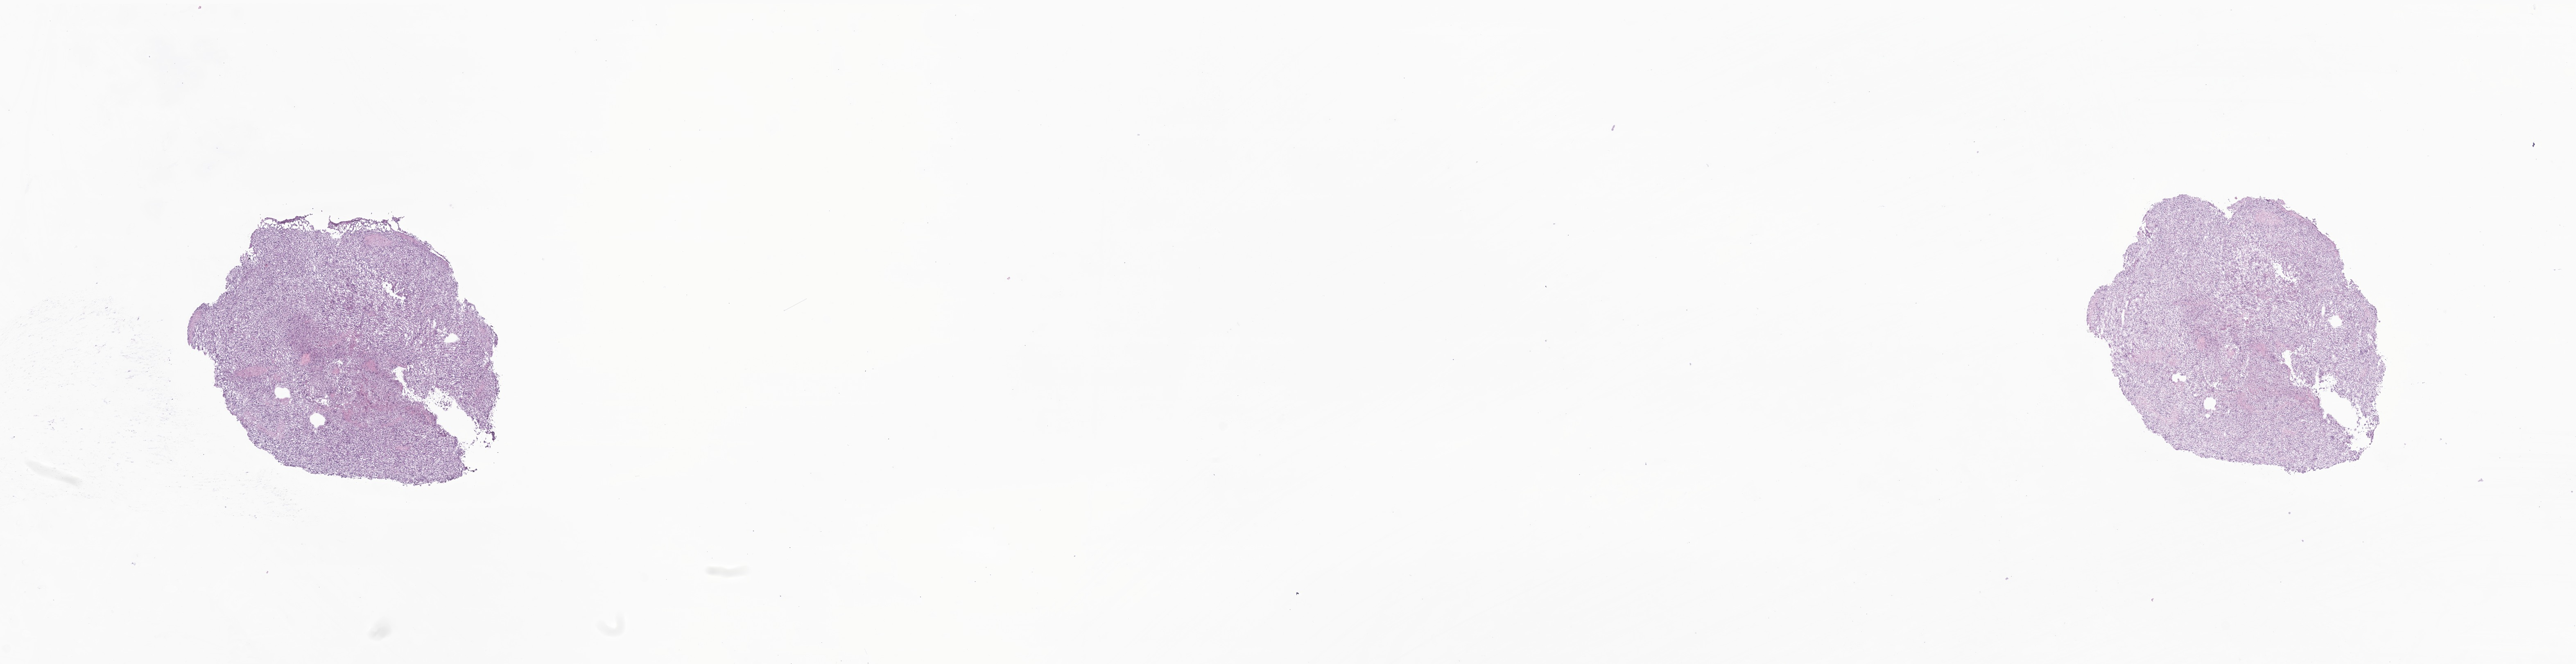
Whole-slide image, hematoxylin and eosin (H&E) stain of tumor tissue from the brain, low-resolution overview of the scanned area, about 26.3 x 6.8 mm, cryosection (OCT / tissue freezing medium). Patient: male, age 201 months (16 years 9 months).
* diagnosis (ICD-O-3 morphology term): Glioma, malignant